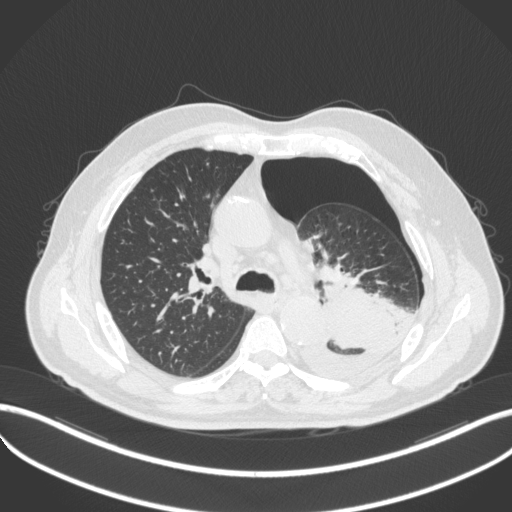
Chest CT, one axial slice. Position 340 of 466 along the scan axis. Reconstruction kernel B31f. Lung window (W 1500 / L -600 HU). 512 × 512 image matrix, field of view 400 × 400 mm. Patient: male, 76 years. Case-level facts recorded for this patient, not image findings: clinical TNM (as recorded): T3 N0 M1b.
Outlined on this slice (bounding box drawn by a radiologist):
- lung tumour (recorded histology: adenocarcinoma): bounding box <290,287,403,378> (left, top, right, bottom; pixels)